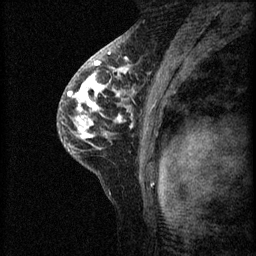
Breast MRI (dynamic contrast-enhanced), one sagittal slice. Slice 42 of 60 in the series (ordered by position). 3 images stored at this slice position (order not interpretable as contrast timing). 1.5 T. TE 4.2 ms, TR 8.2 ms. 2 mm slice thickness. 256 × 256 image matrix, field of view 180 × 180 mm. Female patient, age 41 years.
Structures marked on this image (semi-automatic segmentation, software-assisted and operator-edited):
- analysis volume of interest (the breast-tissue region the enhancement analysis was run in; not a lesion): bounding box [x1, y1, x2, y2] px = [57, 62, 160, 175]
- tumour enhancement mask (voxels above the 70 % enhancement threshold inside the analysis volume of interest): [67, 62, 153, 147]